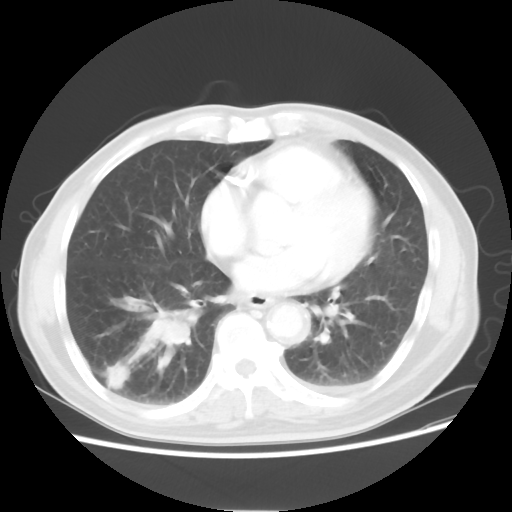
Chest CT, one axial slice. Slice 25 of 58 in the series (ordered by position). 120 kVp. Lung window (W 1500 / L -600 HU). 512 × 512 image matrix. Male patient, age 74 years. From the clinical record (not read from this slice): clinical TNM (as recorded): T1c N1 M1.
Outlined on this slice (bounding box drawn by a radiologist):
- lung tumour (recorded histology: adenocarcinoma): box from (x=128, y=289) to (x=201, y=371) px